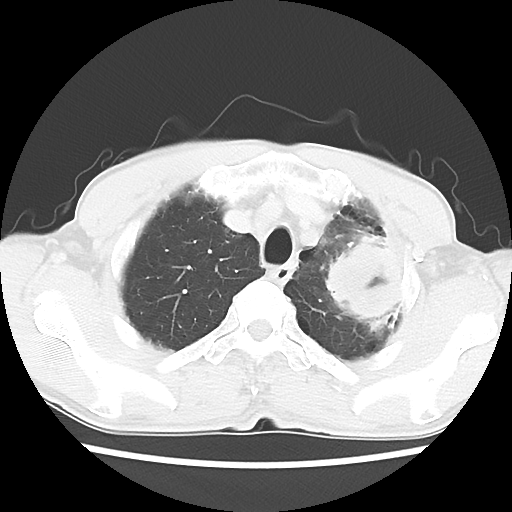
Chest CT, one axial slice. Slice 50 of 60 in the series (ordered by position). Reconstruction kernel LUNG. 120 kVp. Lung window (W 1500 / L -600 HU). 5 mm slice thickness. 512 × 512 image matrix, field of view 308 × 308 mm. Male patient, age 64 years. Case-level facts recorded for this patient, not image findings: clinical TNM (as recorded): T3 N3 M0; histopathological grade: G3.
Structures marked on this image (rectangle marked by the reading radiologist):
- lung tumour (recorded histology: adenocarcinoma): bounding box (x1, y1, x2, y2) in pixels: (321, 225, 410, 333)